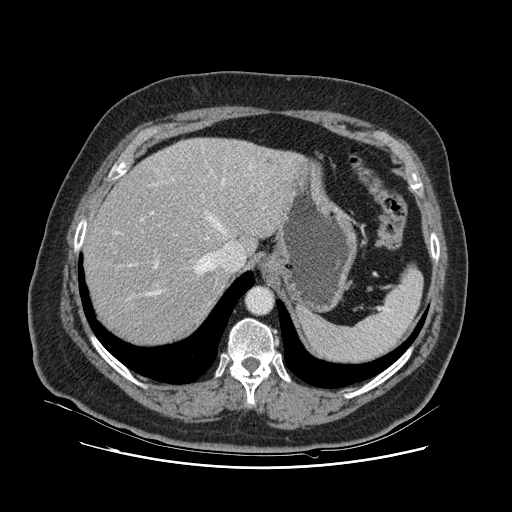
Contrast-enhanced abdominal CT, one axial slice. Position 93 of 132 along the scan axis. Intravenous contrast given. Soft-tissue window (W 400 / L 40 HU). 512 × 512 image matrix, field of view 391 × 391 mm. Female patient, age 73 years. From the clinical record (not read from this slice): diagnosis: colorectal cancer liver metastases, imaged before liver resection; multiple liver metastases: no.
Structures marked on this image (outlined manually by an expert reader):
- hepatic veins: bounding box <115,164,253,295> (left, top, right, bottom; pixels)
- liver: <85,139,301,345>
- planned liver remnant (the part of the liver to remain after resection): <85,160,237,345>
- portal vein (with intrahepatic branches): <150,159,182,269>